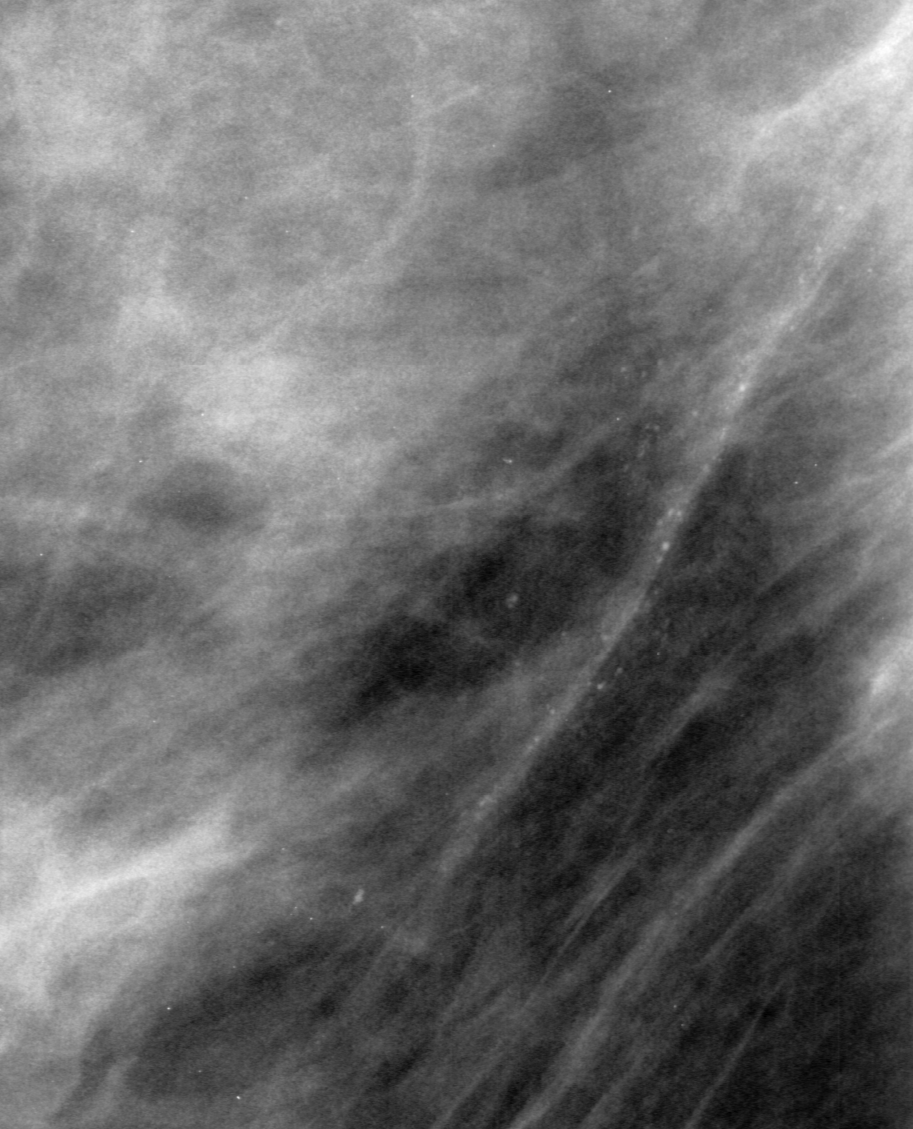
Cropped region of a digitized screen-film mammogram centred on a radiologist-marked abnormality; left breast; MLO view.
Marked abnormality: calcifications, morphology pleomorphic, distribution segmental; BI-RADS assessment category 4; subtlety rating 4 on a 1 (subtle) to 5 (obvious) scale; pathology result (as recorded, not read from the image): benign.